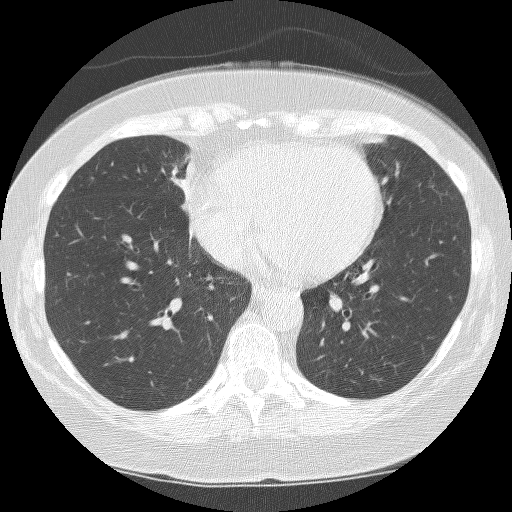
Low-dose screening chest CT, one axial slice; slice 69 of 159 in the series (ordered by position); reconstruction kernel BONE; lung window (W 1500 / L -600 HU); 2.5 mm slice thickness; 512 × 512 image matrix.
Structures marked on this image (expert manual segmentation):
- lesion 1 (tumor, hilum of right lung): box from (x=172, y=159) to (x=196, y=204) px